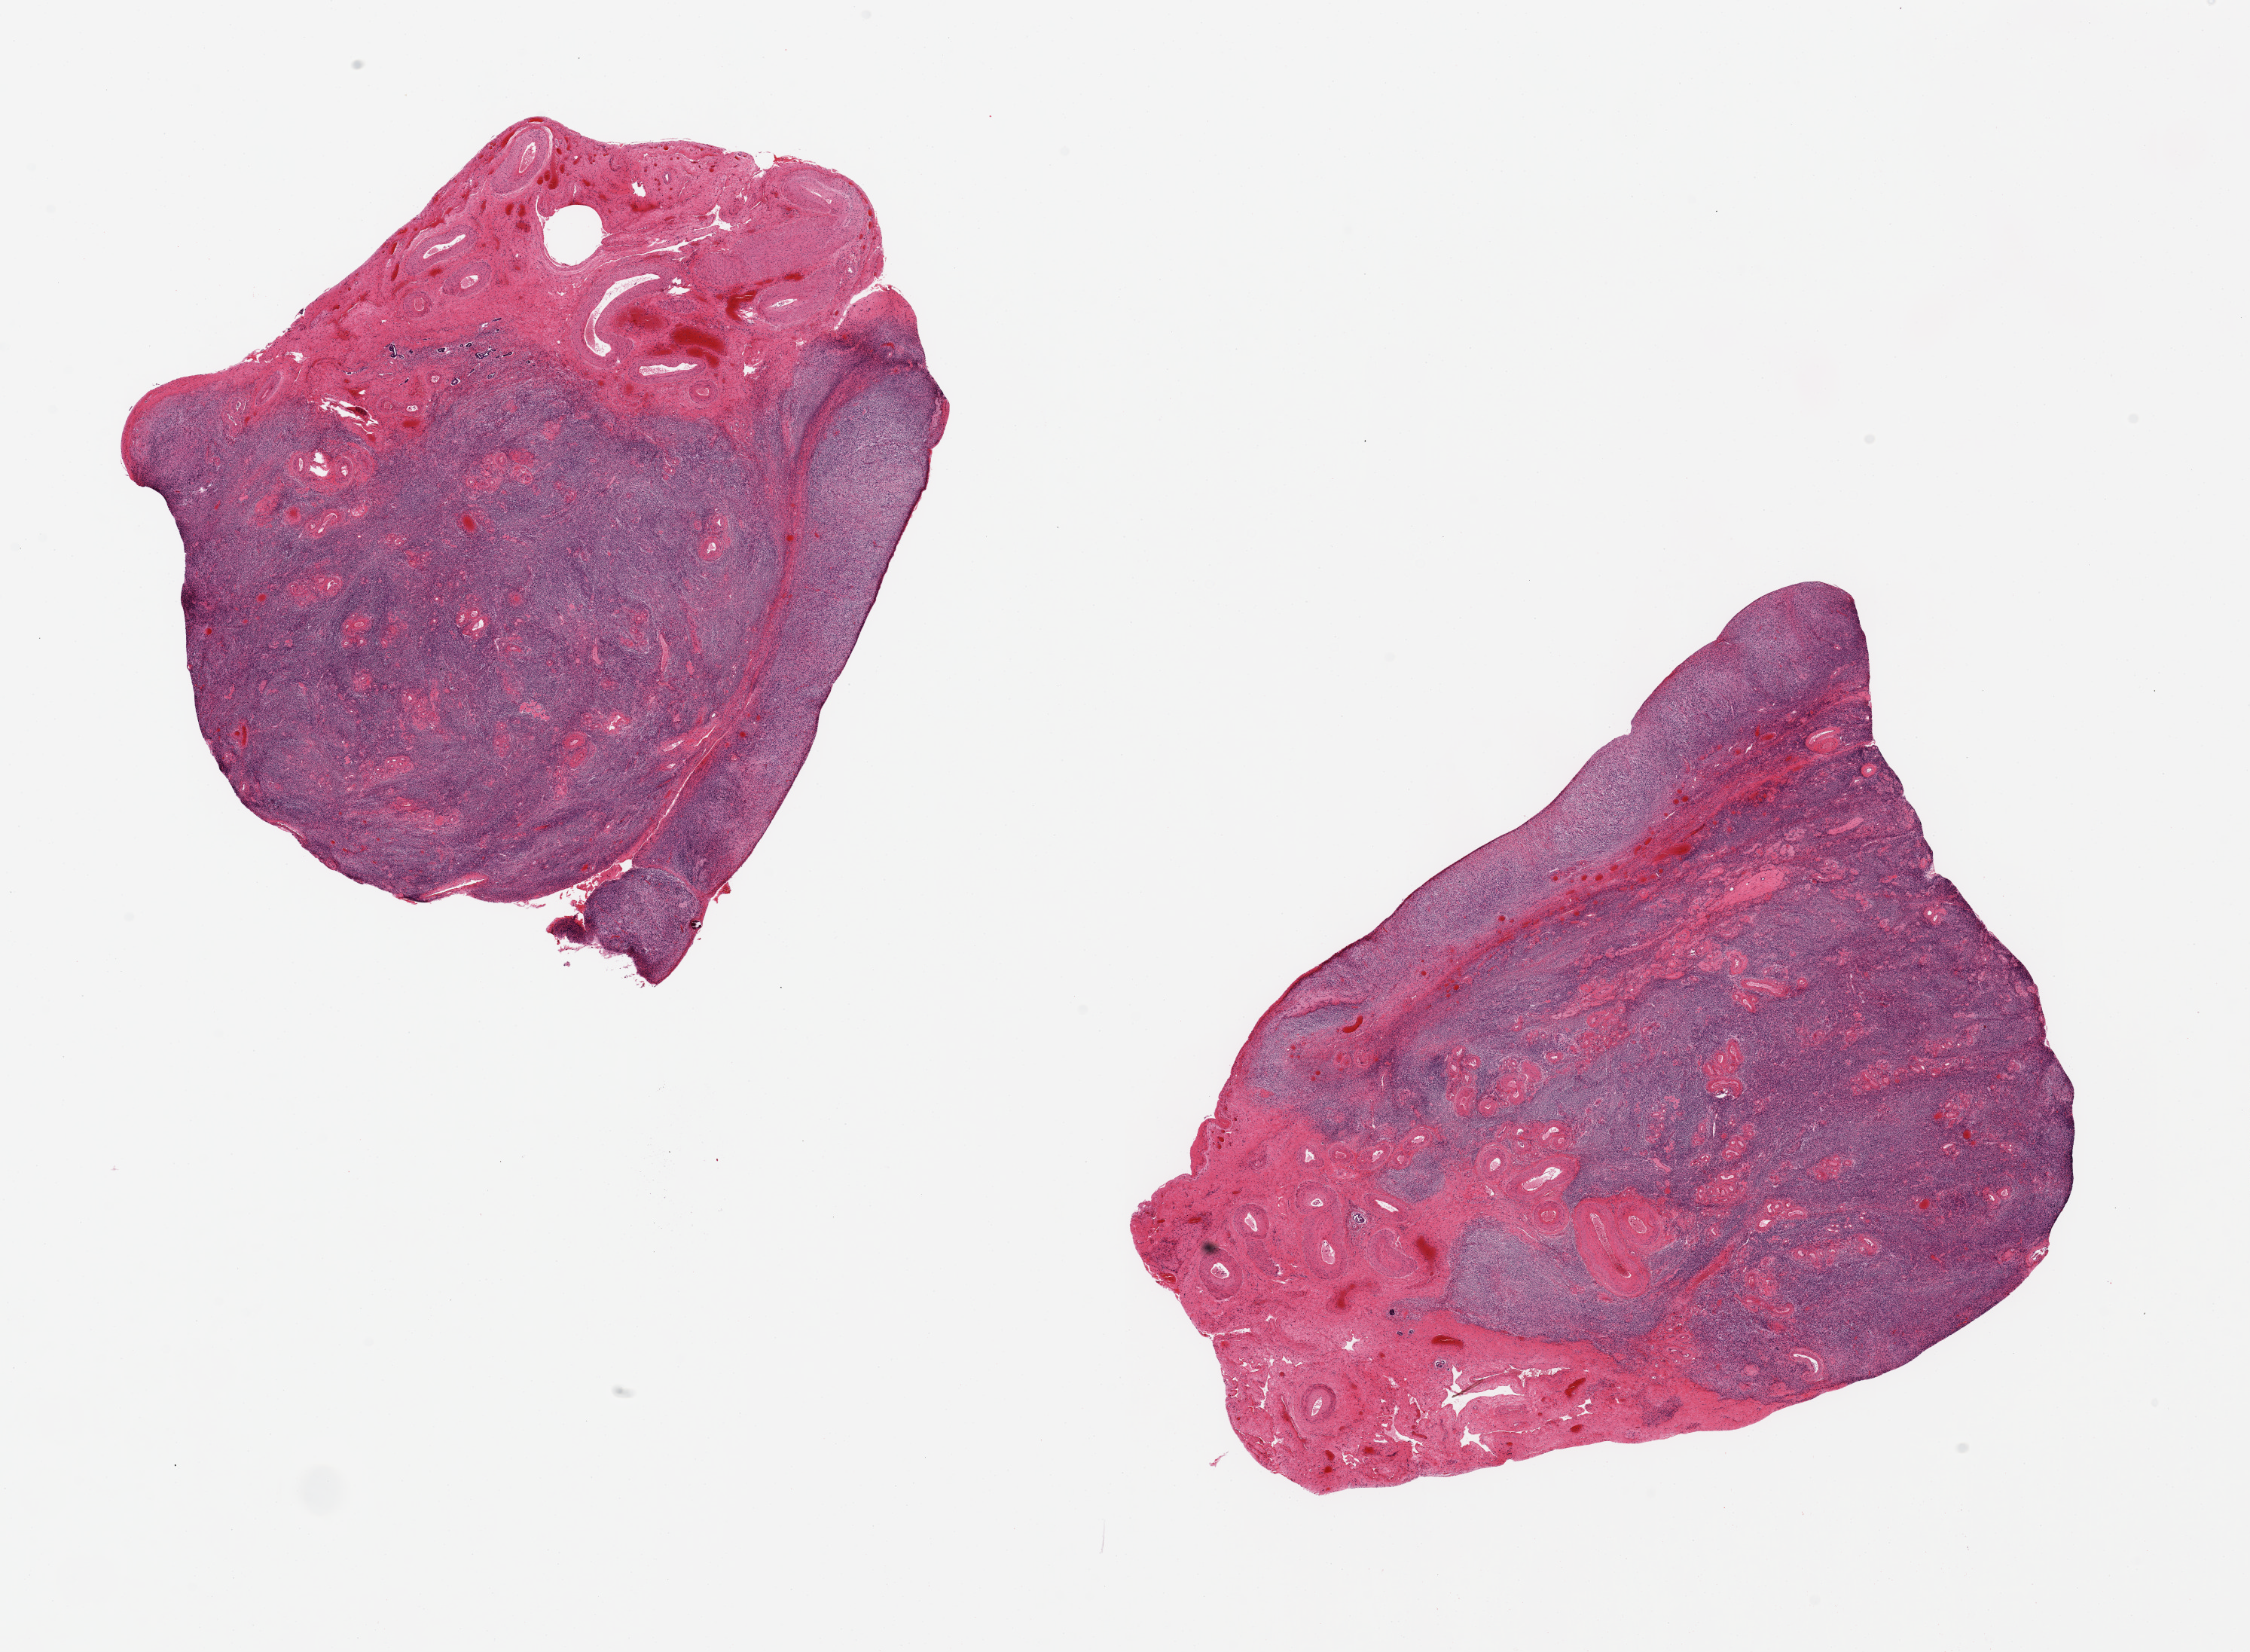
Digitized H&E-stained section, brightfield, whole scanned area (about 23.6 x 17.3 mm) shown as a low-resolution overview. PAXgene-fixed, paraffin-embedded tissue. Sampled site (target tissue): ovary. Tissue donor sample. Donor: female.
• review note (as recorded): 2 pieces ~8x7mm. ~30% of each is hilum. Typical post menopausal atrophy